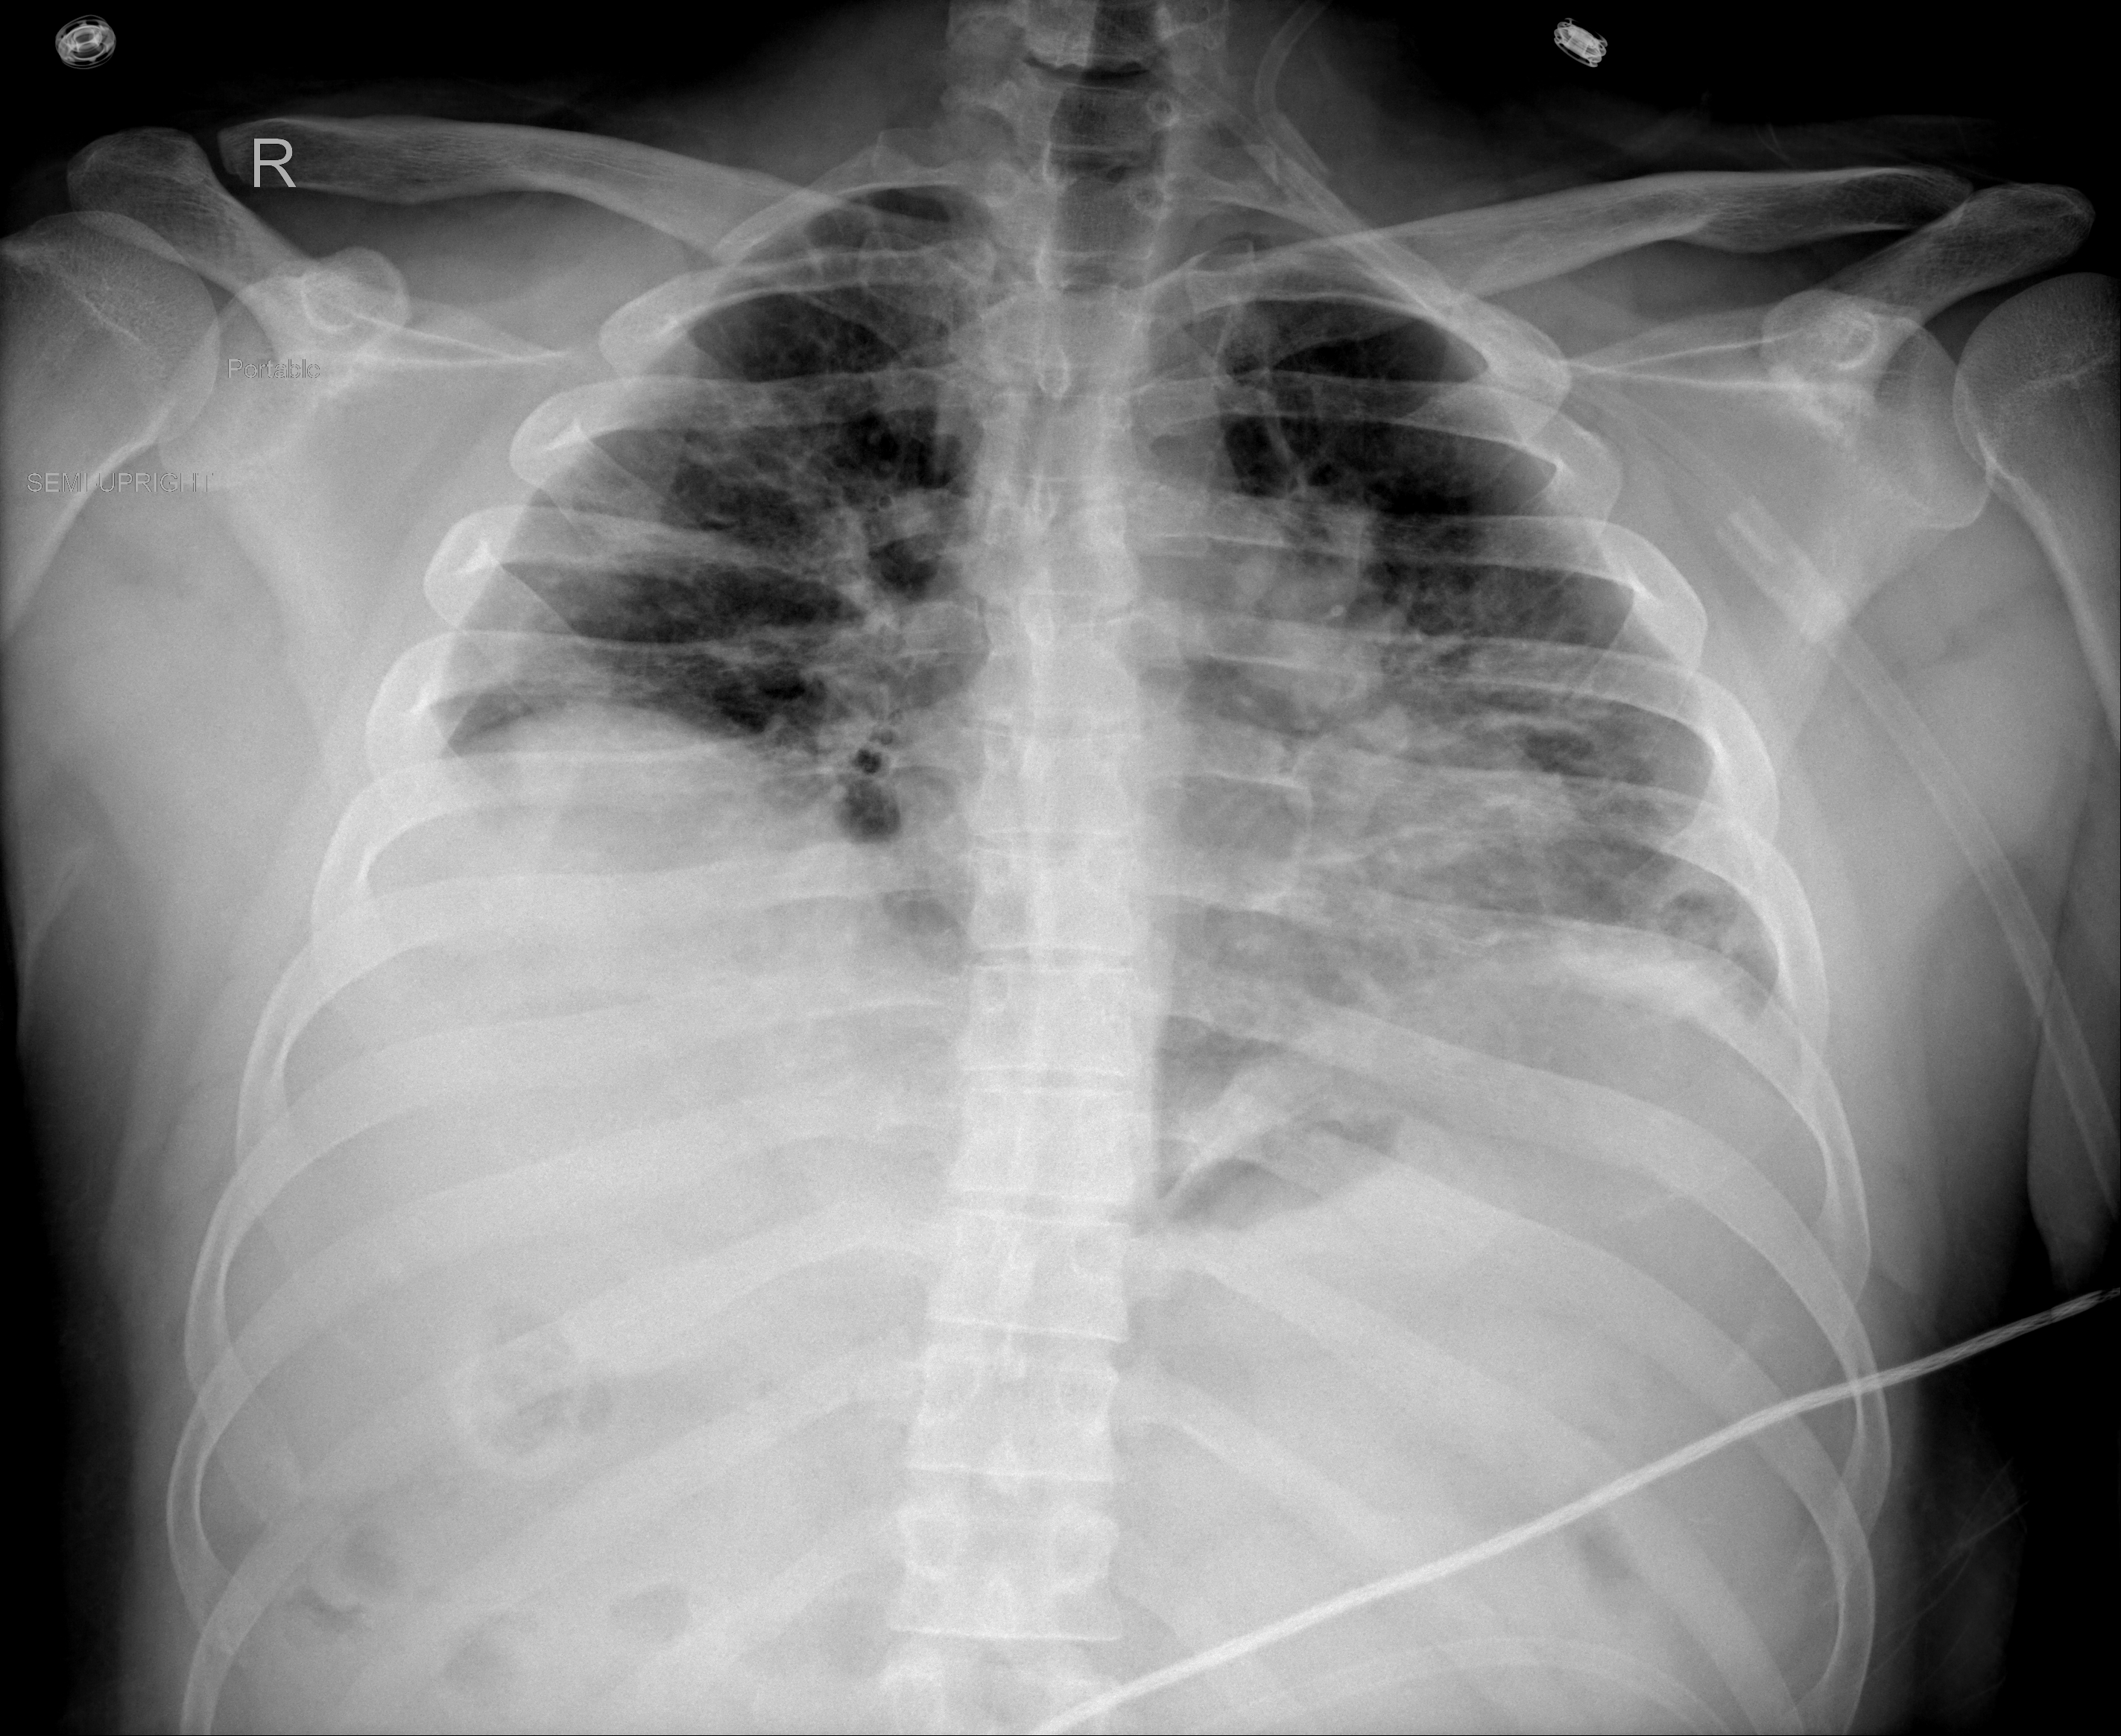
Chest X-ray, PA projection. Male patient, age 39 years; imaged 10 days after the COVID-19 diagnosis.
Radiologist's key findings for this exam: Left lower lobe airspace disease is seen.